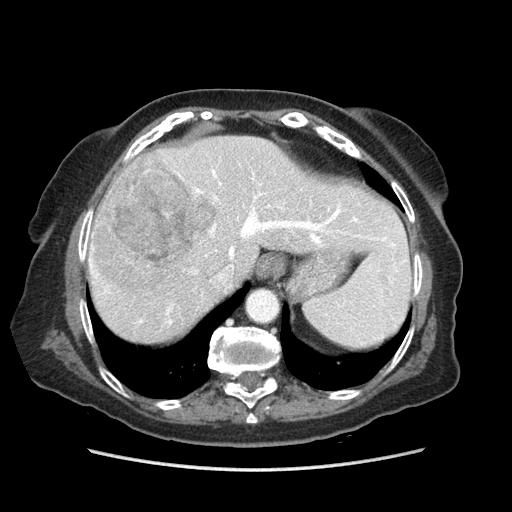
Contrast-enhanced abdominal CT (liver protocol), one axial slice; slice 65 of 89 in the series (ordered by position); reconstruction kernel STANDARD; soft-tissue window (W 400 / L 40 HU); 512 × 512 image matrix, field of view 360 × 360 mm. Case-level facts recorded for this patient, not image findings: diagnosis: hepatocellular carcinoma (patient treated with transarterial chemoembolisation; whether this scan precedes or follows treatment is not stated here); TNM stage (as recorded): Stage-IIIA; Child-Pugh class: A; tumour differentiation: well differentiated; tumour nodularity: multinodular.
Annotated regions visible in this slice (semi-automatic segmentation, software-assisted and operator-edited):
- abdominal aorta: bounding box (x1, y1, x2, y2) in pixels: (247, 291, 277, 321)
- liver parenchyma outside the tumour (the mass and vessels are separate outlines, so this box may not span the whole liver): (84, 136, 404, 342)
- mass: (92, 153, 216, 291)
- liver vessels: (86, 169, 386, 324)